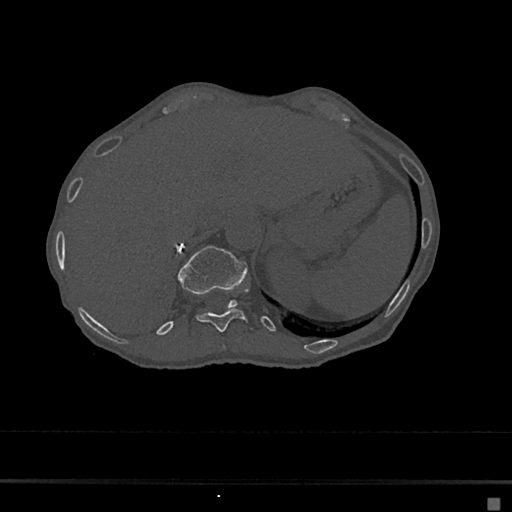
CT including the spine, one axial slice. Slice 160 of 797 in the series (ordered by position). Reconstruction kernel Br40s/3. 120 kVp. Bone window (W 1800 / L 400 HU). 512 × 512 image matrix. Female patient, age 68 years. From the clinical record (not read from this slice): primary cancer: renal.
Outlined on this slice (semi-automatic segmentation, software-assisted and operator-edited):
- T10 vertebra: box from (x=221, y=346) to (x=225, y=351) px
- T11 vertebra: (x=196, y=288)–(x=253, y=332)
- T12 vertebra: (x=177, y=246)–(x=248, y=308)